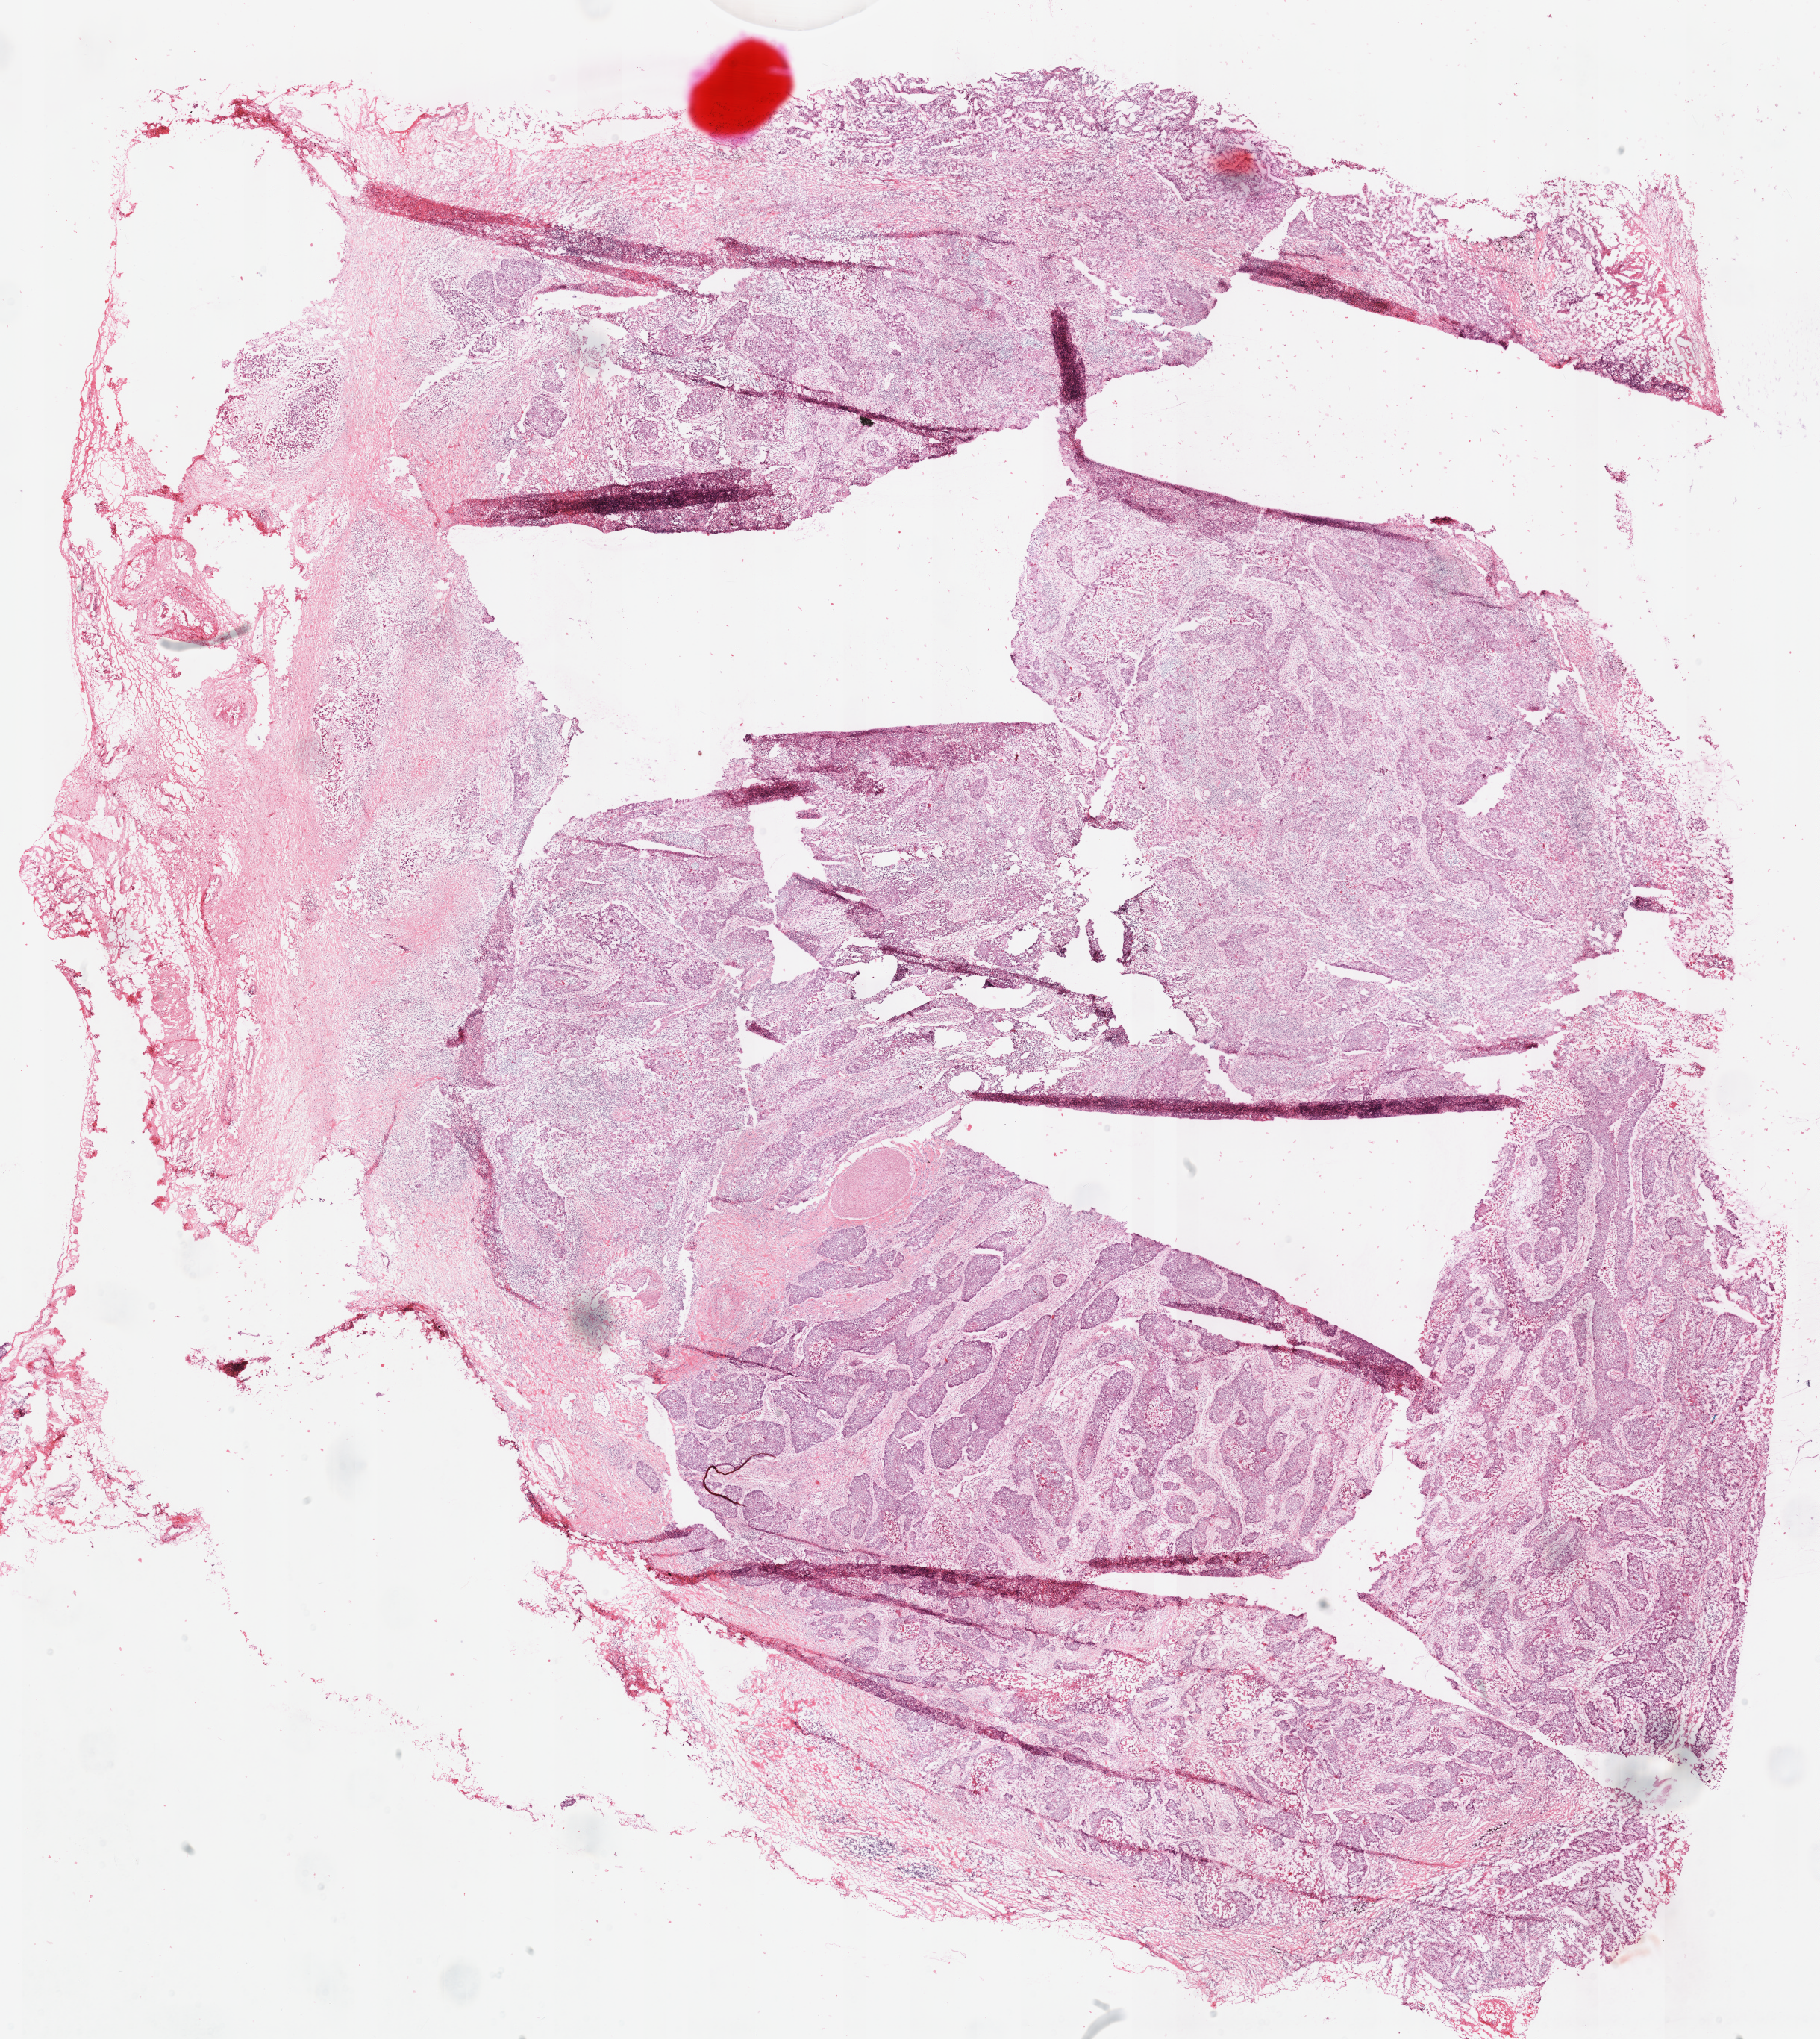
H&E-stained whole-slide image — whole scanned area (about 19.2 x 21.5 mm, slide scanned at 40x) shown as a low-resolution overview, frozen section from the top of the tissue portion, sample: primary tumour, lung. Male, age 65 years at initial diagnosis. Composition of this section per pathologist review: tumour cells 80%, tumour nuclei 65%, normal cells 0%, stromal cells 20%, necrosis 0%. Inflammatory infiltration, as recorded: lymphocyte infiltration 20%, monocyte infiltration 0%, neutrophil infiltration 9%.
AJCC pathologic stage: IB (7th edition). Diagnosis: Squamous cell carcinoma, NOS (upper lobe, lung).